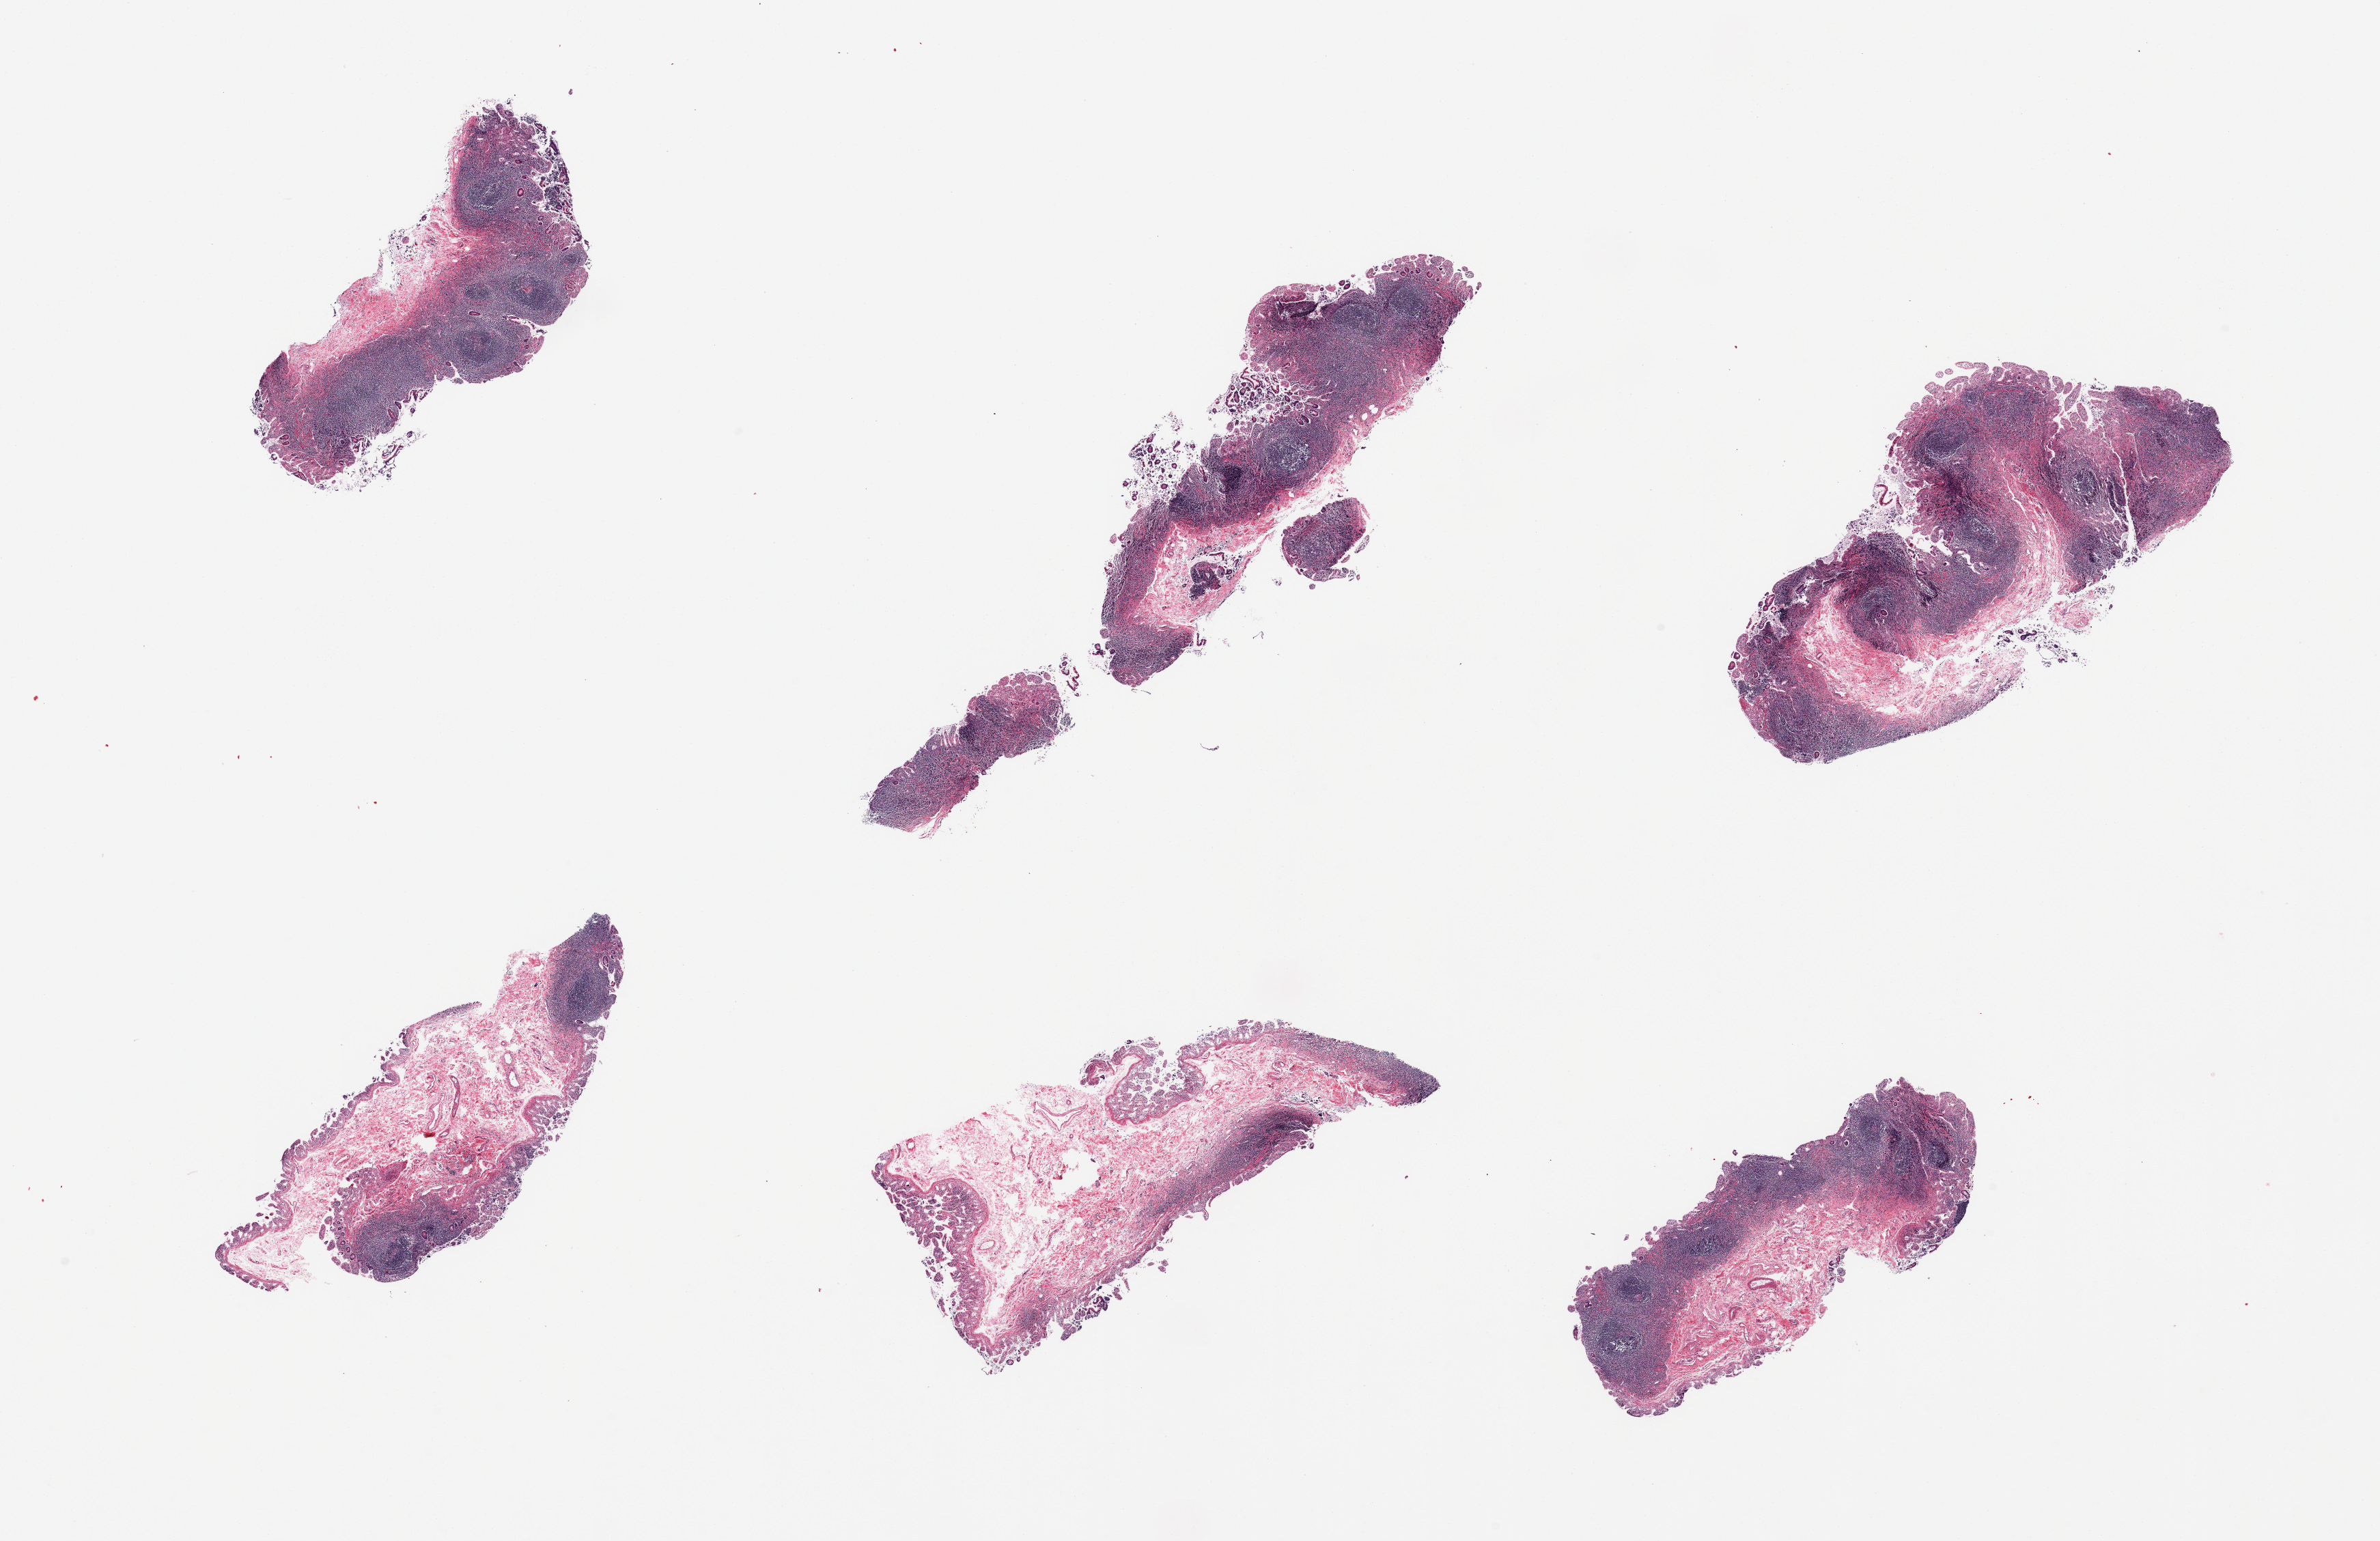
Haematoxylin and eosin whole-slide image, whole scanned area (about 27.6 x 17.9 mm) shown as a low-resolution overview. PAXgene-fixed paraffin-embedded (PFPE) section. Sampled site (target tissue): ileum. Tissue donor sample. Donor sex: male.
• pathologist's review note for this sample: 6 pieces; moderately autolyzed mucosa, but with good lymphoid component